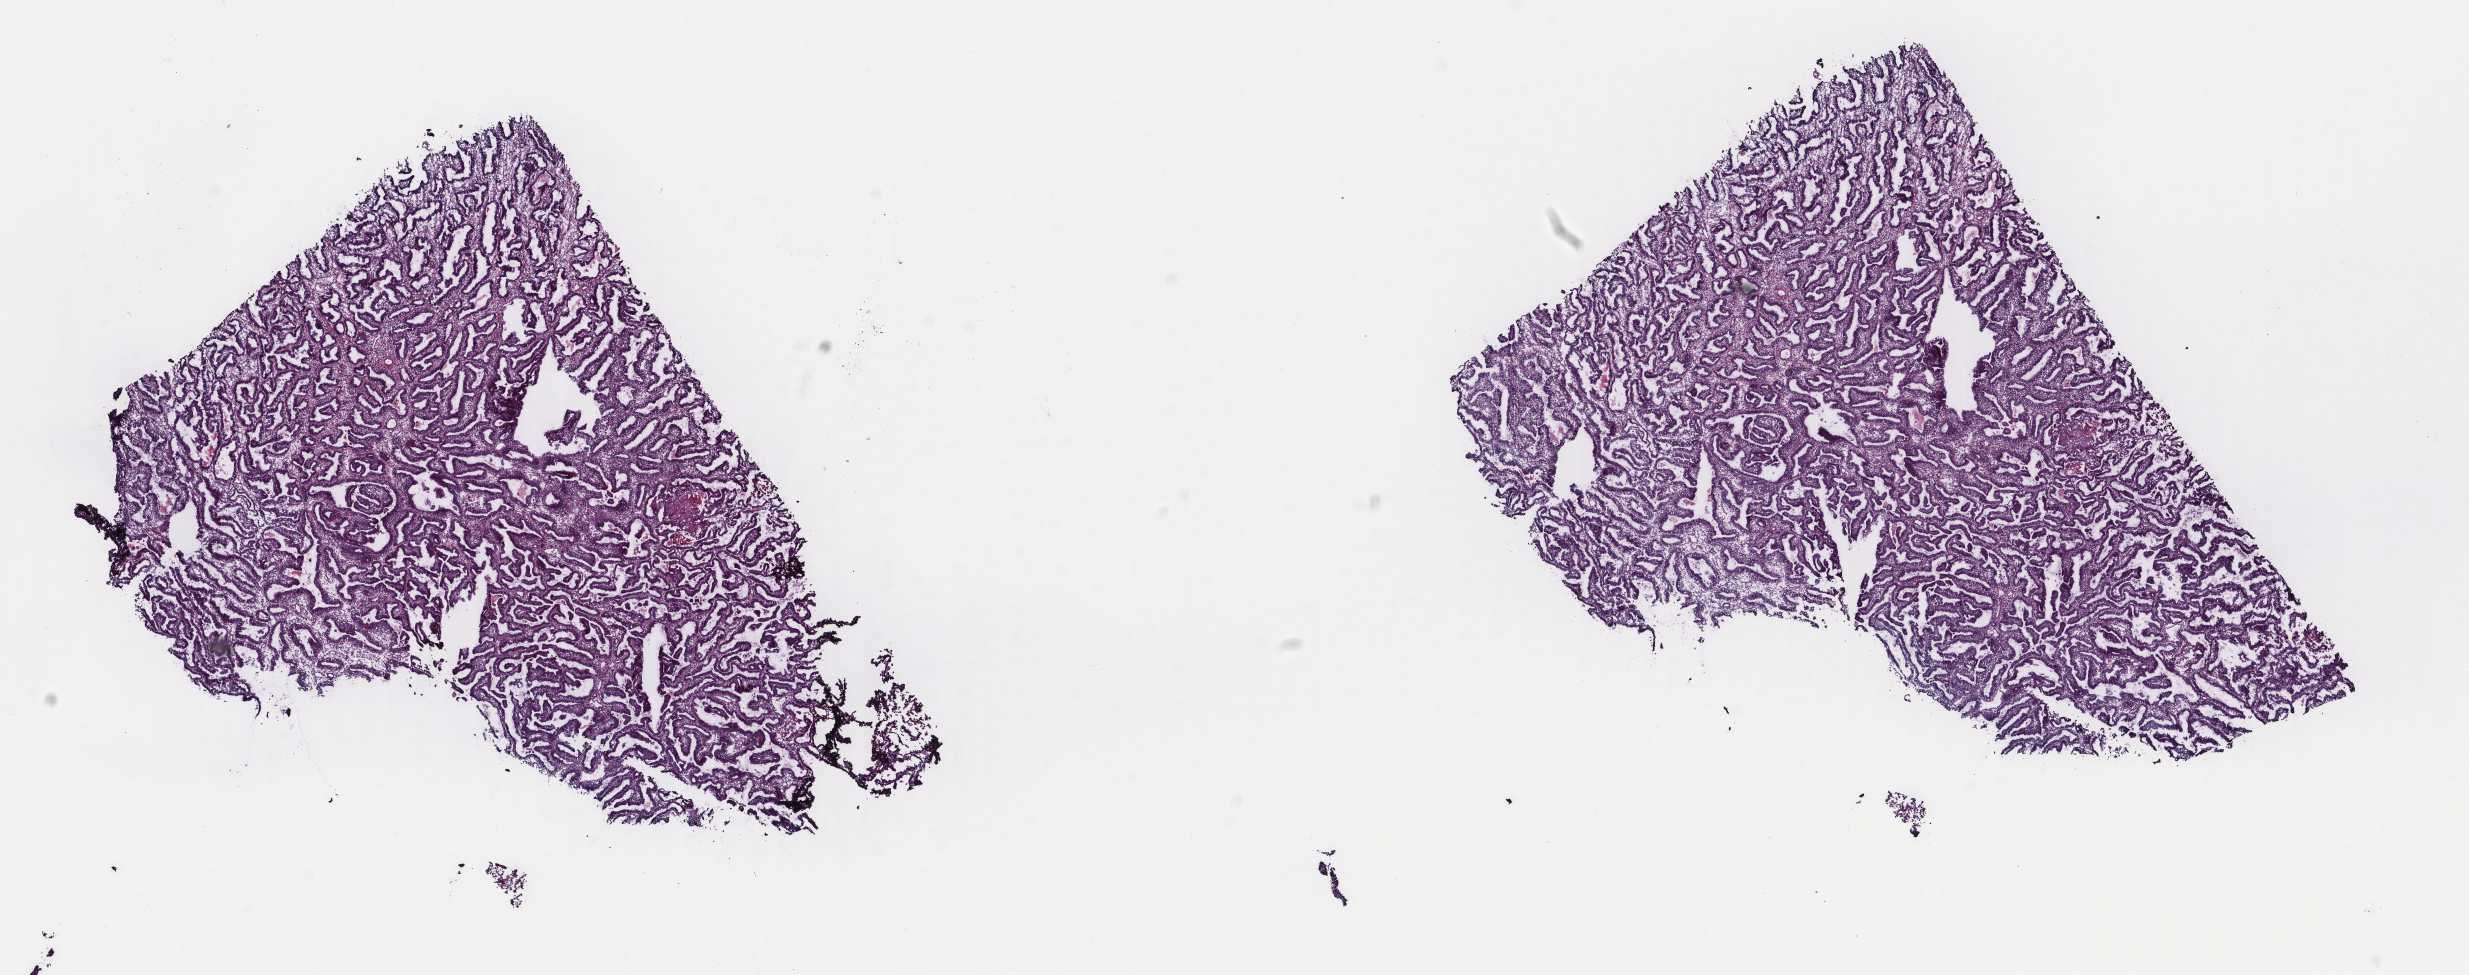
Whole-slide histology image, Hematoxylin and eosin (H&E) stained, whole scanned area (about 19.6 x 7.7 mm, from a 40x scan) shown as a low-resolution overview, frozen section, sample: primary tumour, uterus. Female, age 54 years at initial diagnosis. Histologic grade: G2 (moderately differentiated). Pathologist review of this section (percent, as recorded): tumour cells 100%, tumour nuclei 65%, normal cells 0%, stromal cells 0%, necrosis 0%. Inflammatory infiltration, as recorded: lymphocyte infiltration 0%, monocyte infiltration 0%, neutrophil infiltration 0%.
Pathologic diagnosis: Endometrioid adenocarcinoma, NOS (endometrium). Lymph nodes positive (case pathology): 0 of 29 examined. FIGO stage: IA.